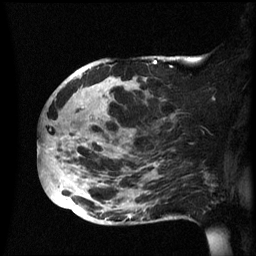
Breast MRI (dynamic contrast-enhanced), one sagittal slice; dynamic contrast-enhanced series, image 2 of 3 at this slice position (ordered by acquisition); 1.5 T; TE 4.2 ms, TR 8.4 ms; 256 × 256 image matrix, field of view 230 × 230 mm. Female patient, age 49 years.
Structures marked on this image (semi-automatic segmentation, software-assisted and operator-edited):
- analysis volume of interest (the breast-tissue region the enhancement analysis was run in; not a lesion): bounding box <39,56,174,225> (left, top, right, bottom; pixels)
- tumour enhancement mask (voxels above the 70 % enhancement threshold inside the analysis volume of interest): <45,61,157,156>